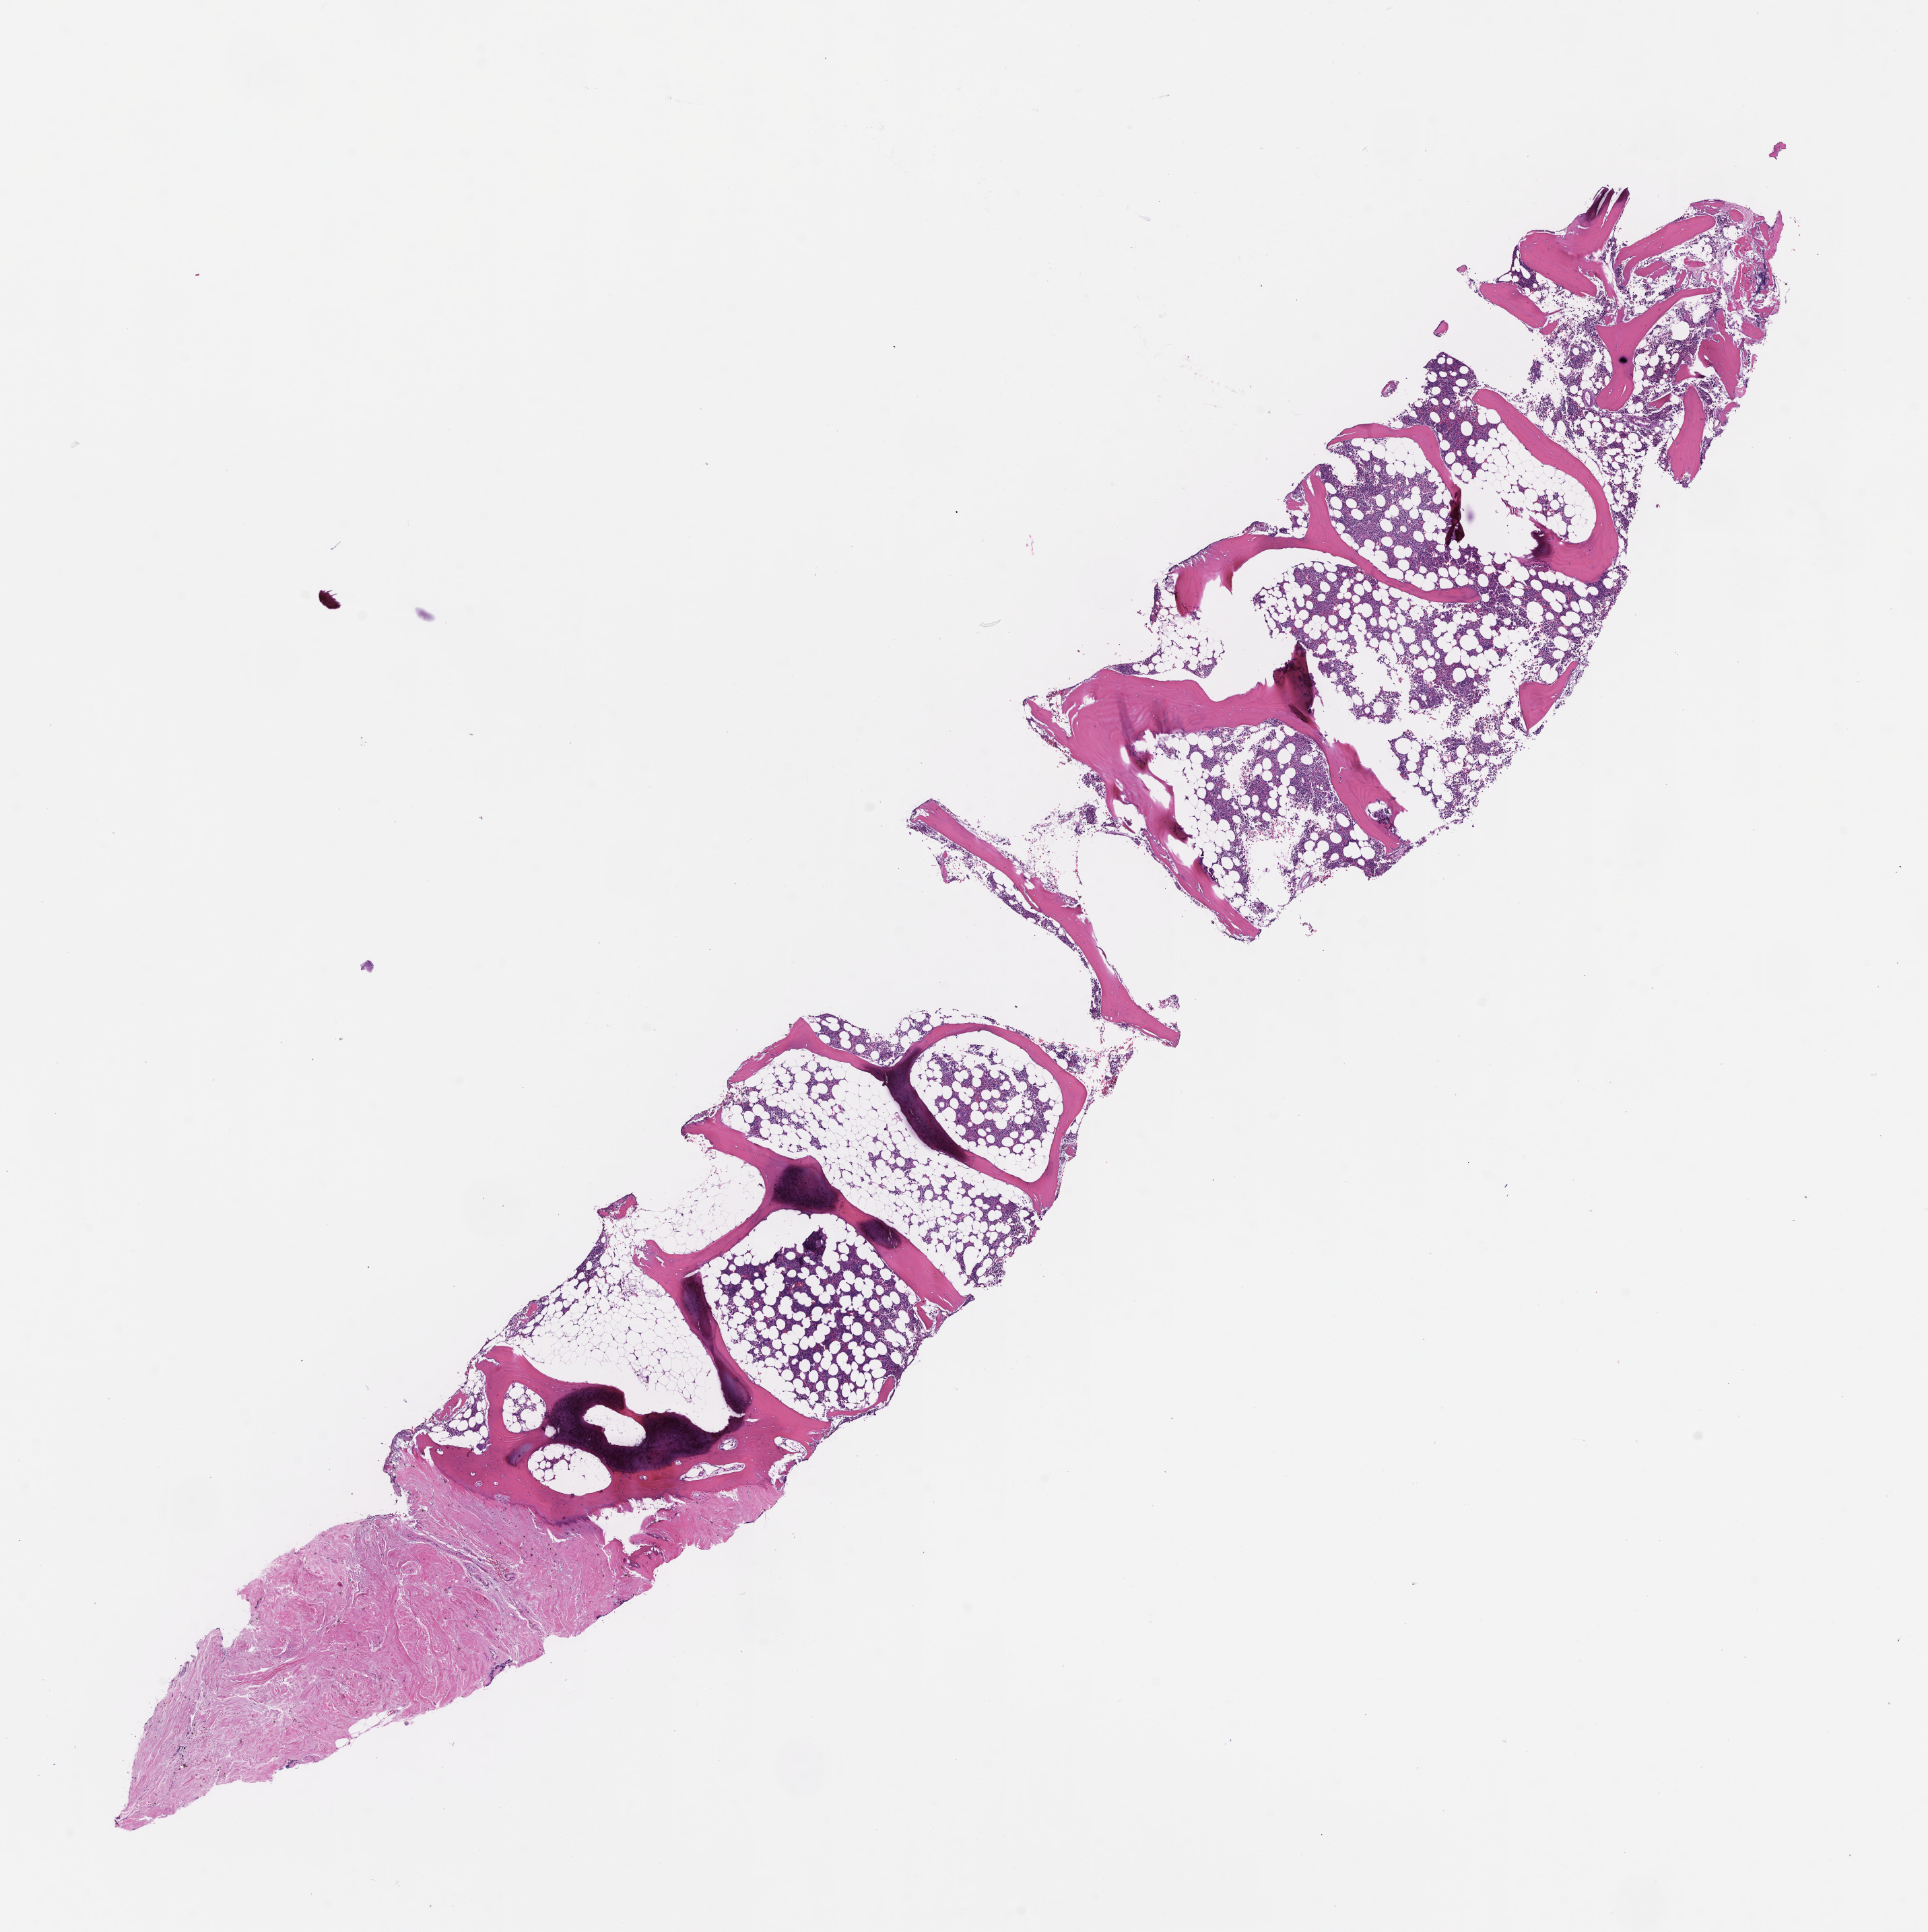
Digitized haematoxylin and eosin-stained section — low-resolution overview of the scanned area, about 11.6 x 11.6 mm; FFPE section; tissue site: bone marrow; specimen time point: archival tissue. Patient sex: male.
This section: primary tumor. Diagnosis: Plasma Cell Myeloma.